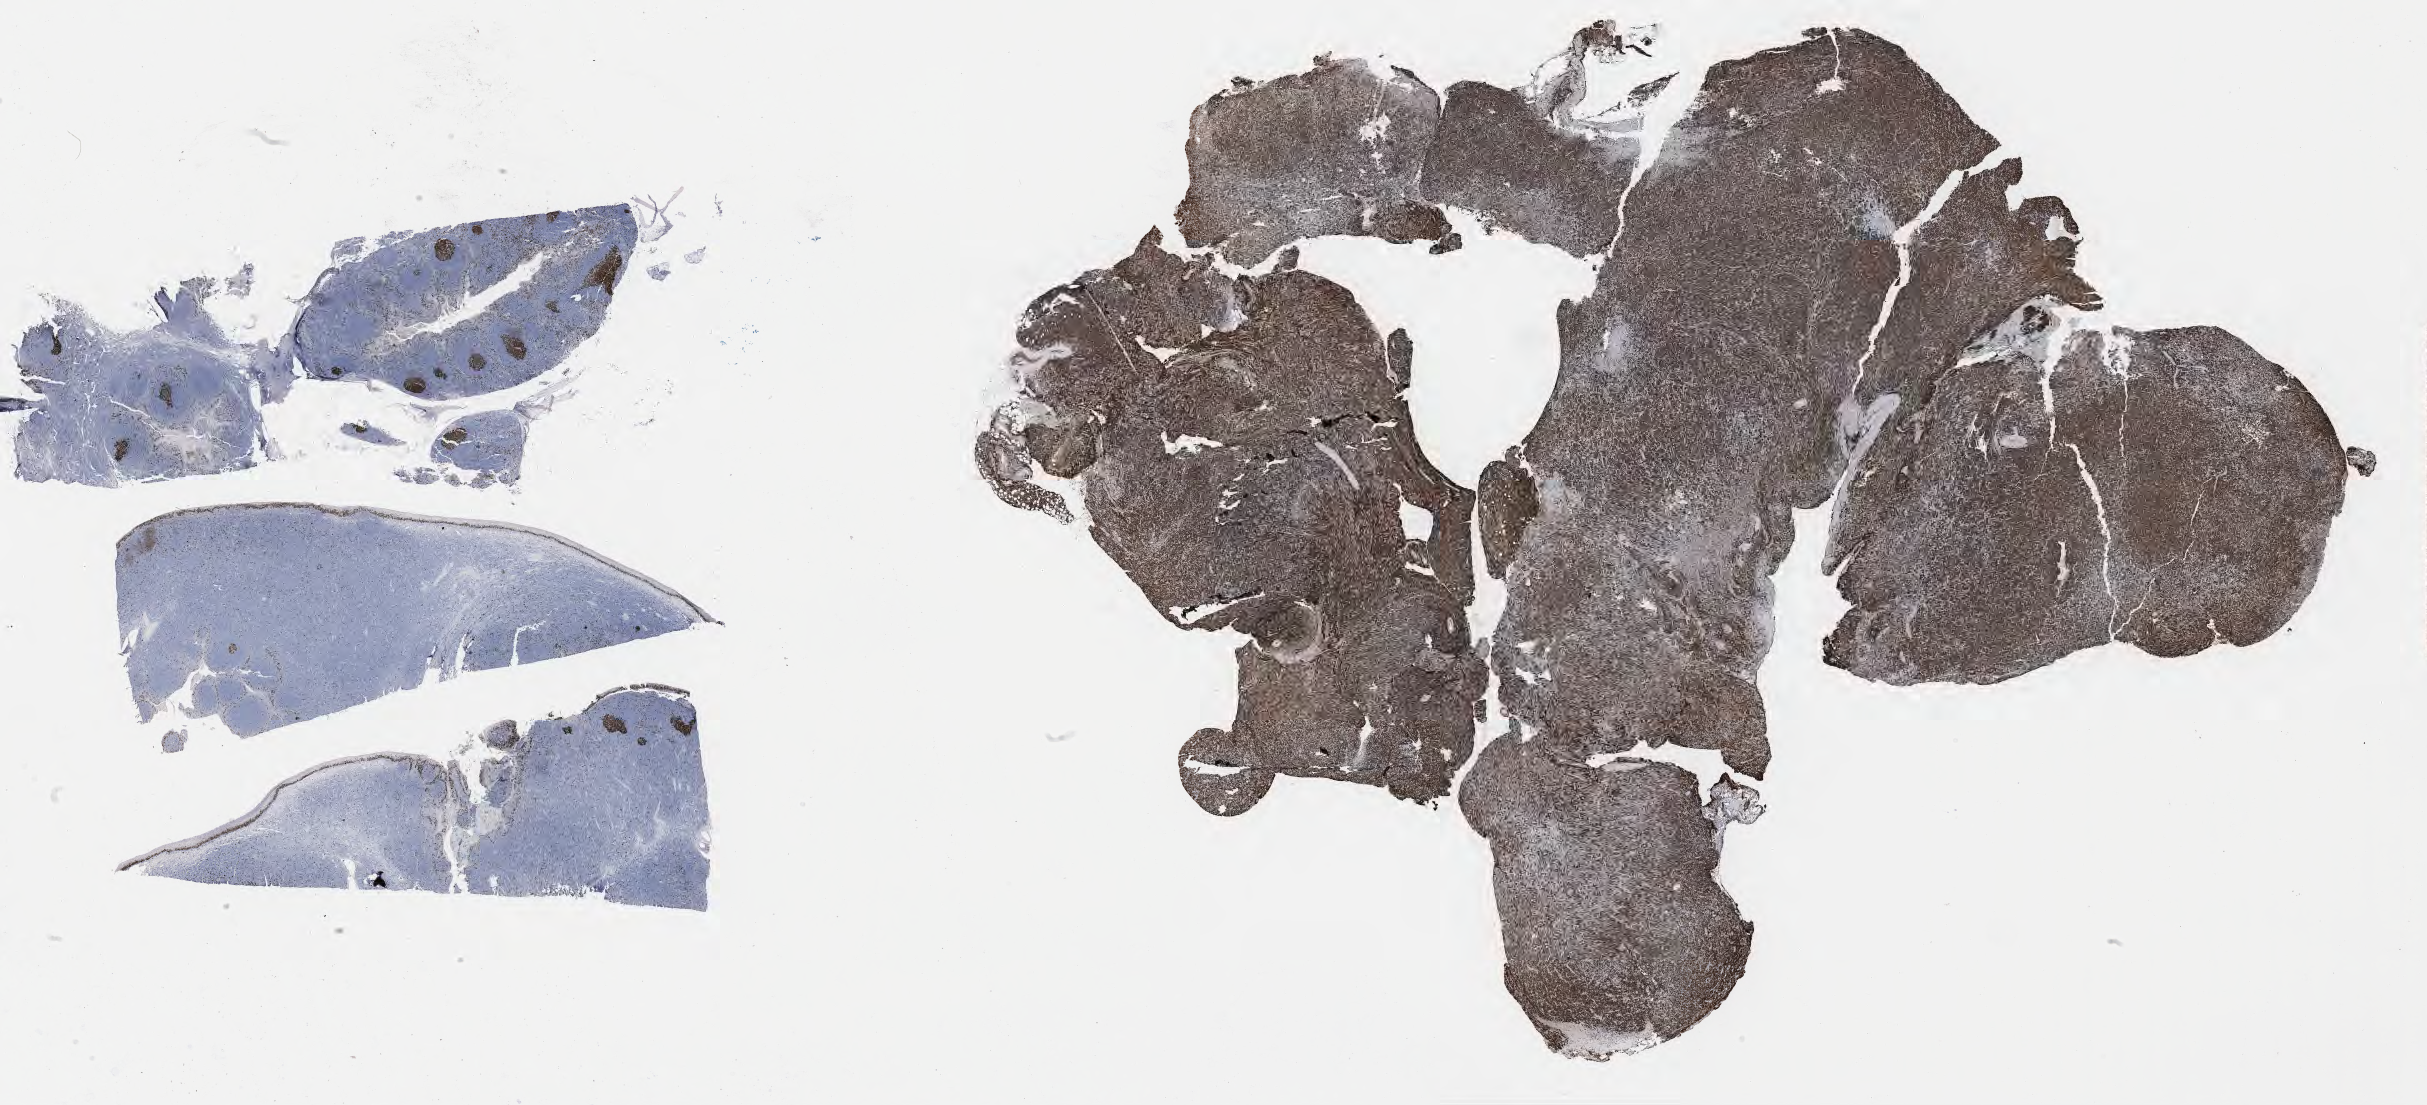
IHC for Ki-67, whole-slide image, a low-resolution overview of the entire scanned area, about 39.3 x 17.9 mm; tumor tissue; site: soft tissue of abdomen. Female, age 8 years at initial diagnosis.
Histologic diagnosis: Burkitt lymphoma, NOS.